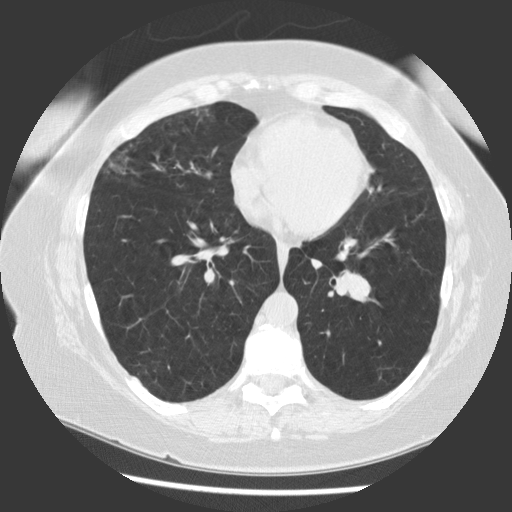
Low-dose screening chest CT, one axial slice. Position 56 of 130 along the scan axis. 120 kVp. Lung window (W 1500 / L -600 HU). 2.5 mm slice thickness. 512 × 512 image matrix, field of view 340 × 340 mm.
Structures marked on this image (manually delineated by an expert):
- lesion 1 (tumor, hilum of left lung): bounding box (x1, y1, x2, y2) in pixels: (341, 274, 370, 302)